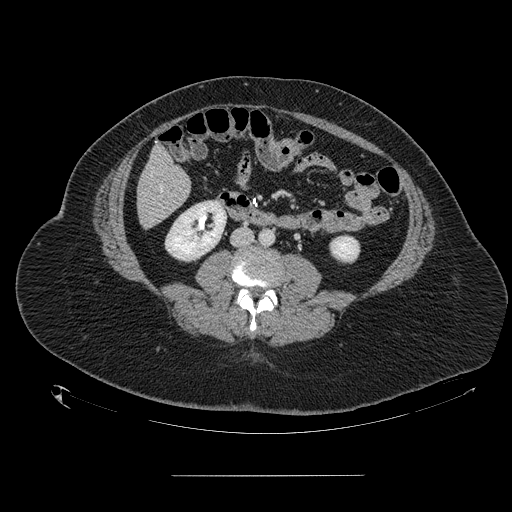
Contrast-enhanced abdominal CT, one axial slice. Slice 32 of 164 in the series (ordered by position). Intravenous contrast given. Soft-tissue window (W 400 / L 40 HU). 2.5 mm slice thickness. 512 × 512 image matrix, field of view 495 × 495 mm. Female patient, age 52 years. From the clinical record (not read from this slice): diagnosis: colorectal cancer liver metastases, imaged before liver resection; multiple liver metastases: yes; largest metastasis: 3.5 cm; disease in both lobes: no.
Outlined on this slice (outlined manually by an expert reader):
- hepatic veins: box from (x=159, y=186) to (x=162, y=188) px
- liver: (x=138, y=148)–(x=191, y=228)